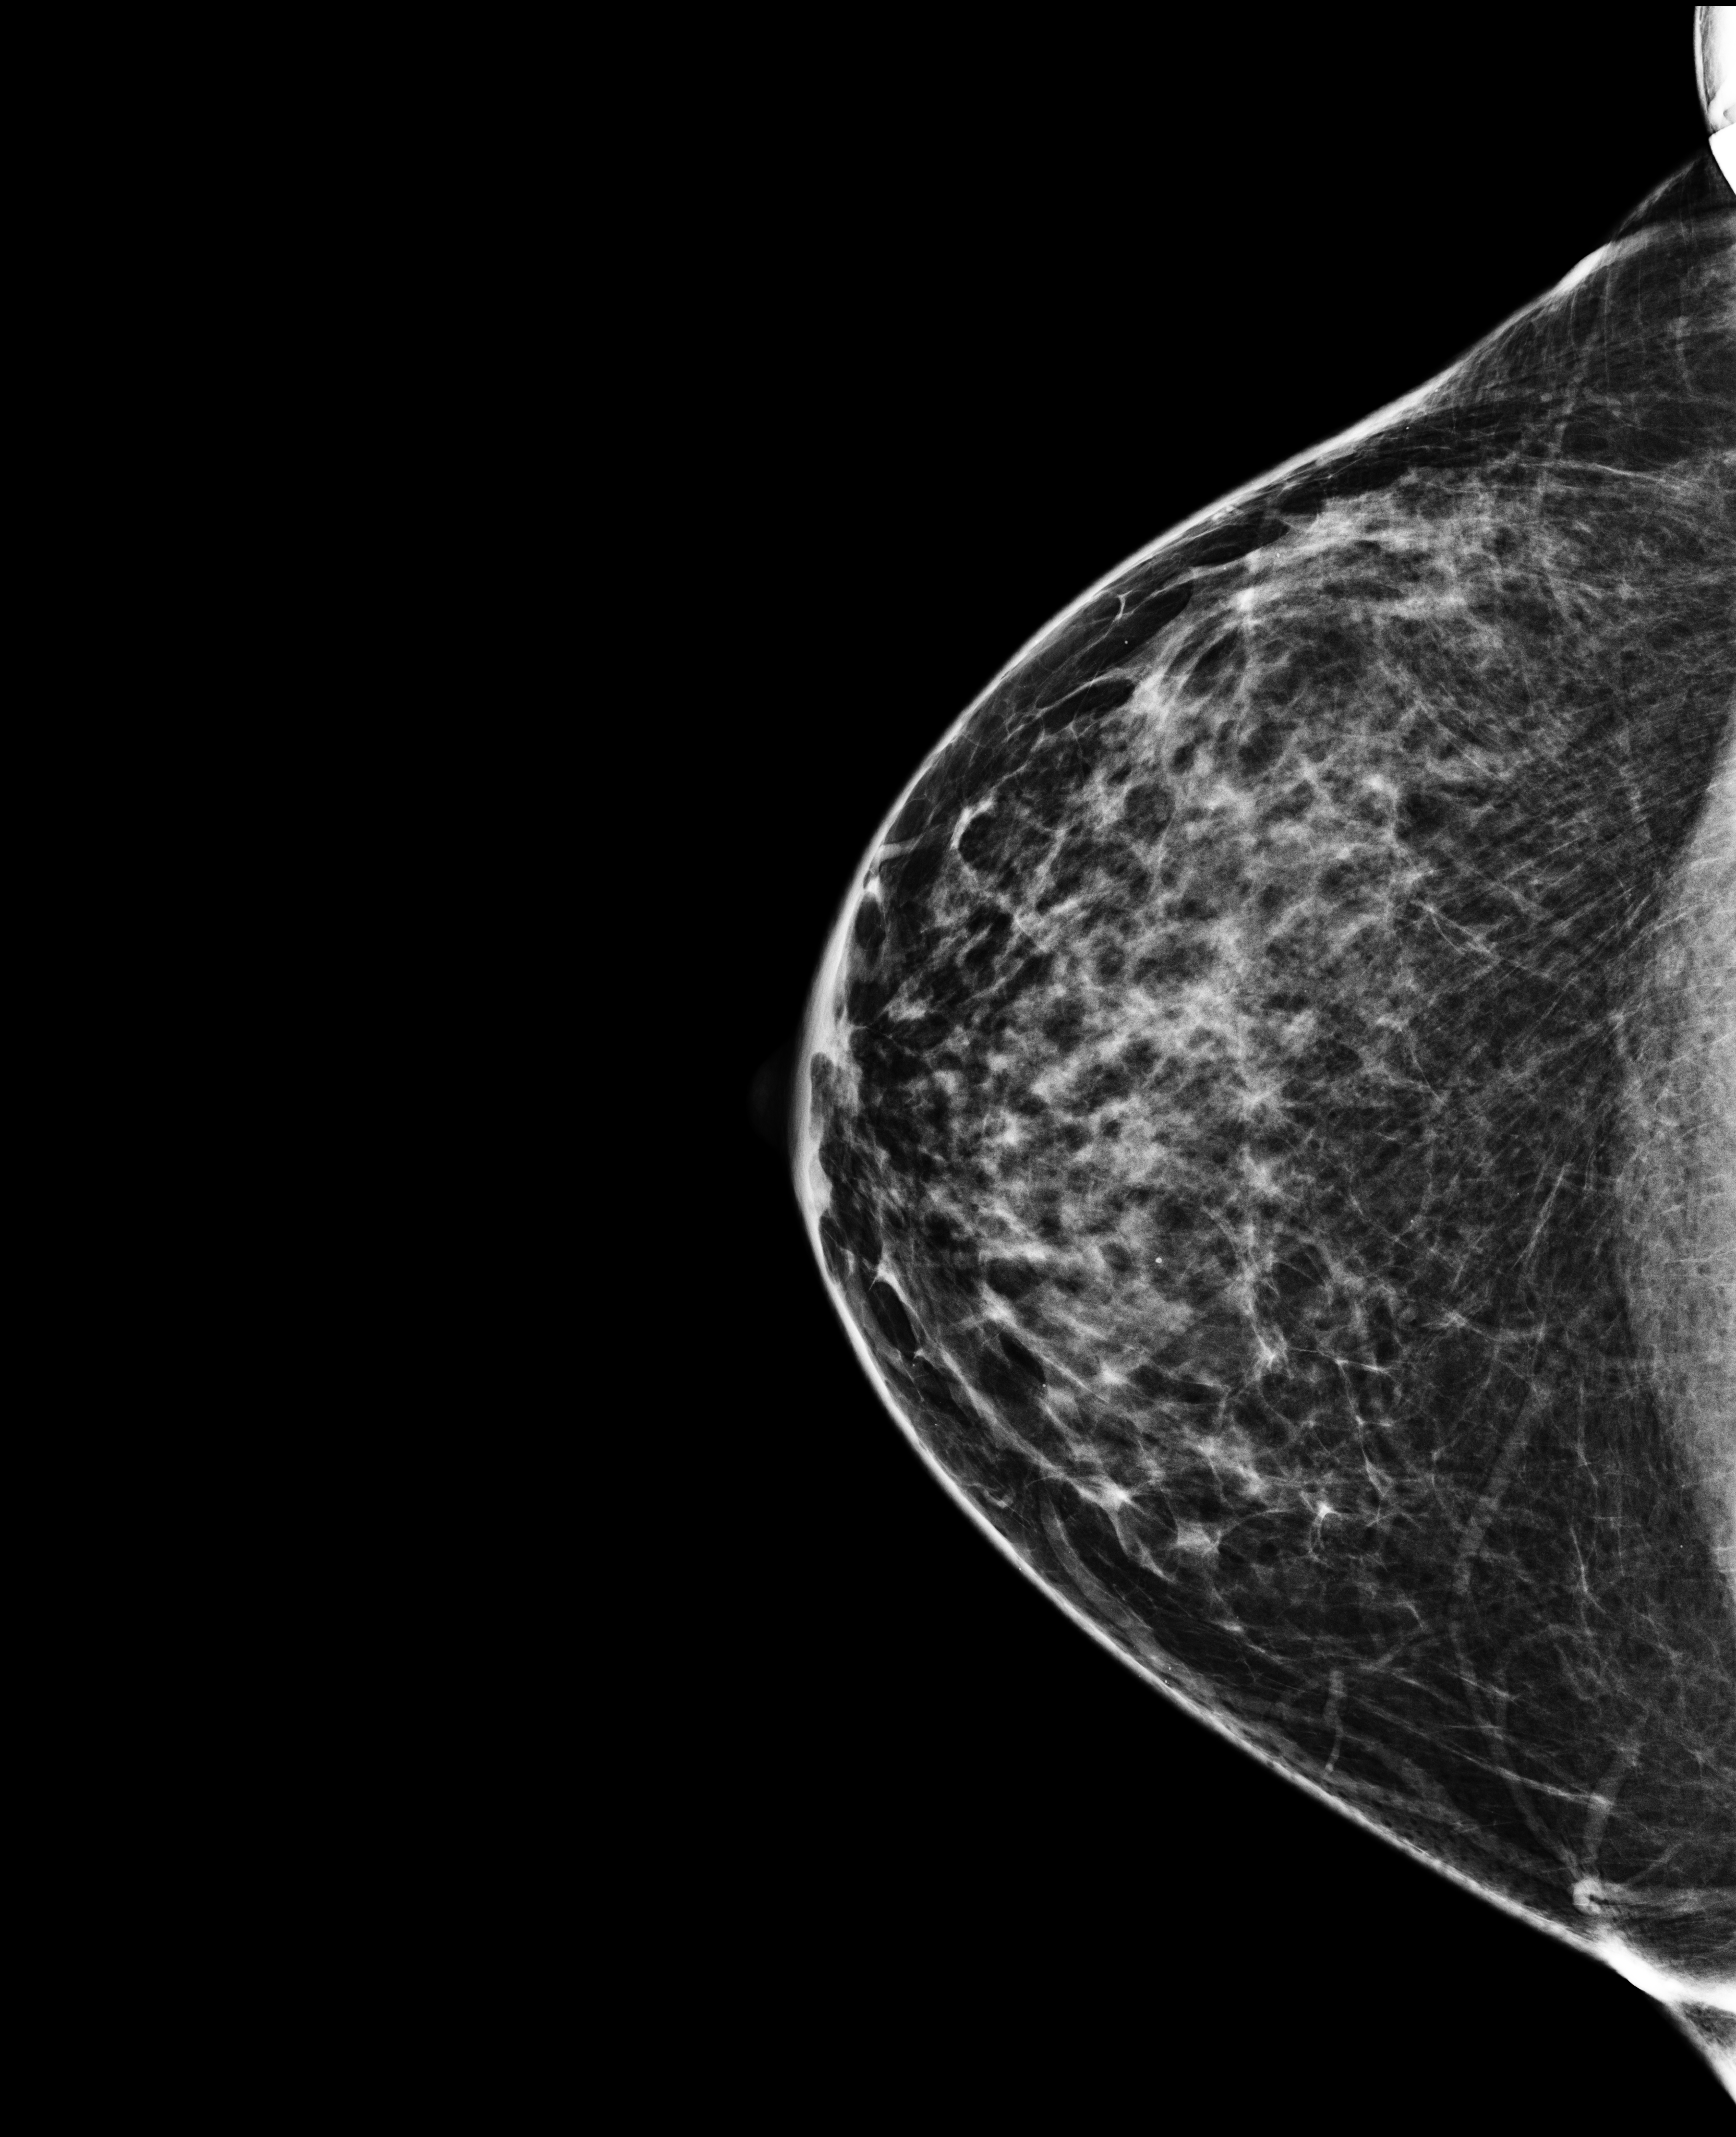
Screening examination, compressed breast thickness 59 mm, system: Selenia Dimensions. Female patient, age 49 years.
Image type: full-field digital mammogram. Breast: right. Projection: cranio-caudal projection.